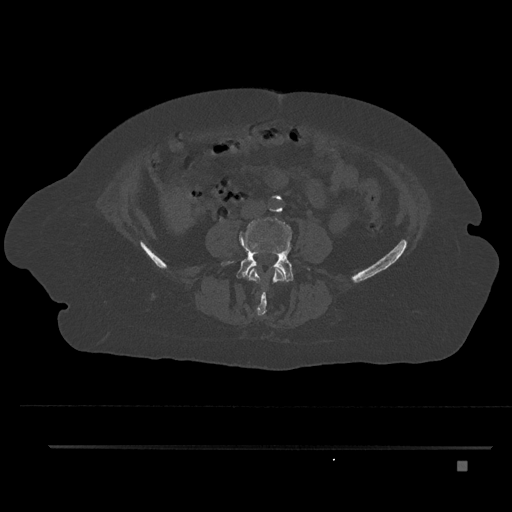
CT including the spine, one axial slice; slice 95 of 797 in the series (ordered by position); reconstruction kernel Br40s/3; 120 kVp; bone window (W 1800 / L 400 HU); 0.5 mm slice thickness; 512 × 512 image matrix, field of view 437 × 437 mm. Patient: female, 76 years. From the clinical record (not read from this slice): primary cancer: lung.
Annotated regions visible in this slice (semi-automatically segmented with operator editing):
- L3 vertebra: bounding box [x1, y1, x2, y2] px = [248, 267, 285, 315]
- L4 vertebra: [221, 217, 294, 283]